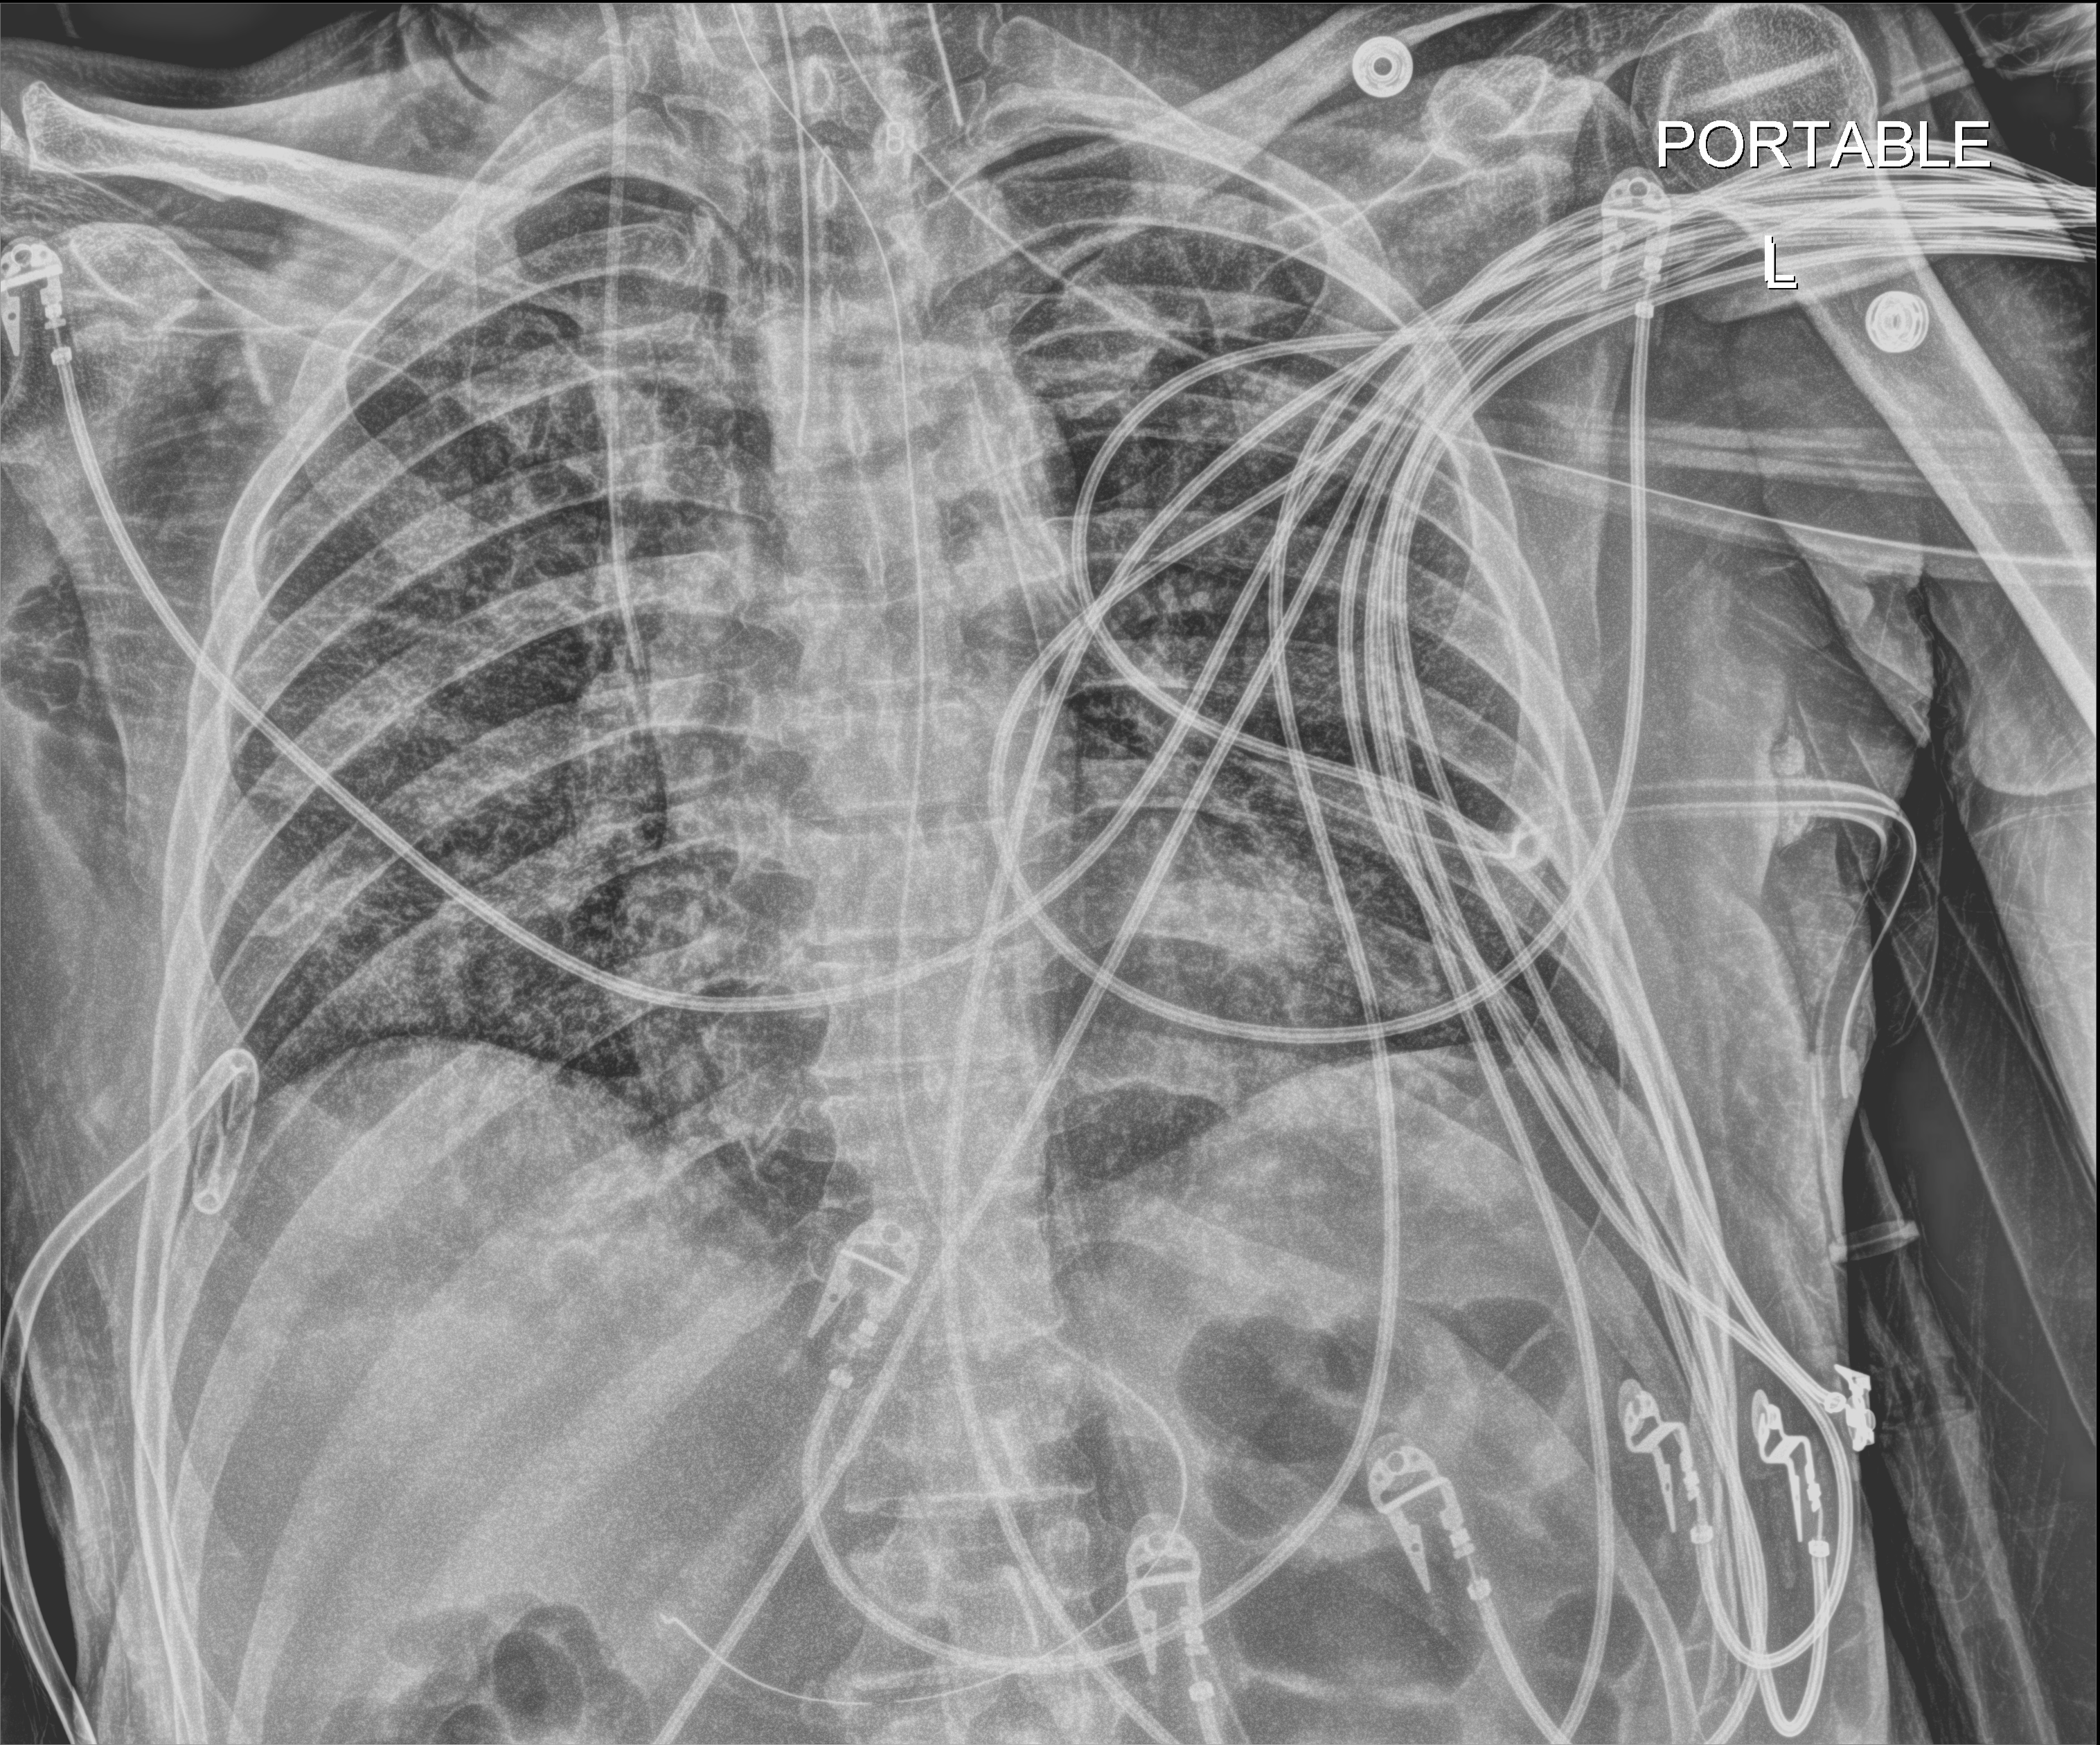
Chest X-ray (portable), anteroposterior (AP) projection. Patient hospitalised with COVID-19; male, aged 18–59 years.
Hospital-stay facts (about this admission, not read from this image; timing relative to this image not recorded): COPD (admission record): no.